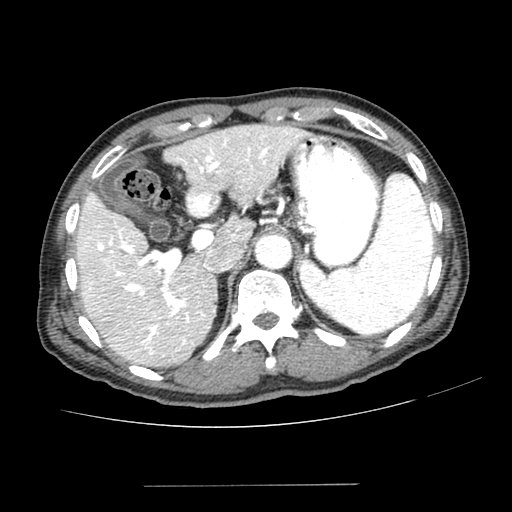
Contrast-enhanced abdominal CT (liver protocol), one axial slice. Slice 159 of 187 in the series (ordered by position). Reconstruction kernel SOFT. 100 kVp. One of 2 acquisitions stored at this slice position. Soft-tissue window (W 400 / L 40 HU). 512 × 512 image matrix, field of view 360 × 360 mm. From the clinical record (not read from this slice): diagnosis: hepatocellular carcinoma (patient treated with transarterial chemoembolisation; whether this scan precedes or follows treatment is not stated here); TNM stage (as recorded): Stage-I; Child-Pugh class: A; tumour nodularity: uninodular; tumour size: 1.6 cm.
Annotated regions visible in this slice (semi-automatic segmentation, software-assisted and operator-edited):
- liver parenchyma outside the tumour (the mass and vessels are separate outlines, so this box may not span the whole liver): bounding box (x1, y1, x2, y2) in pixels: (76, 124, 302, 366)
- liver vessels: (82, 130, 298, 355)